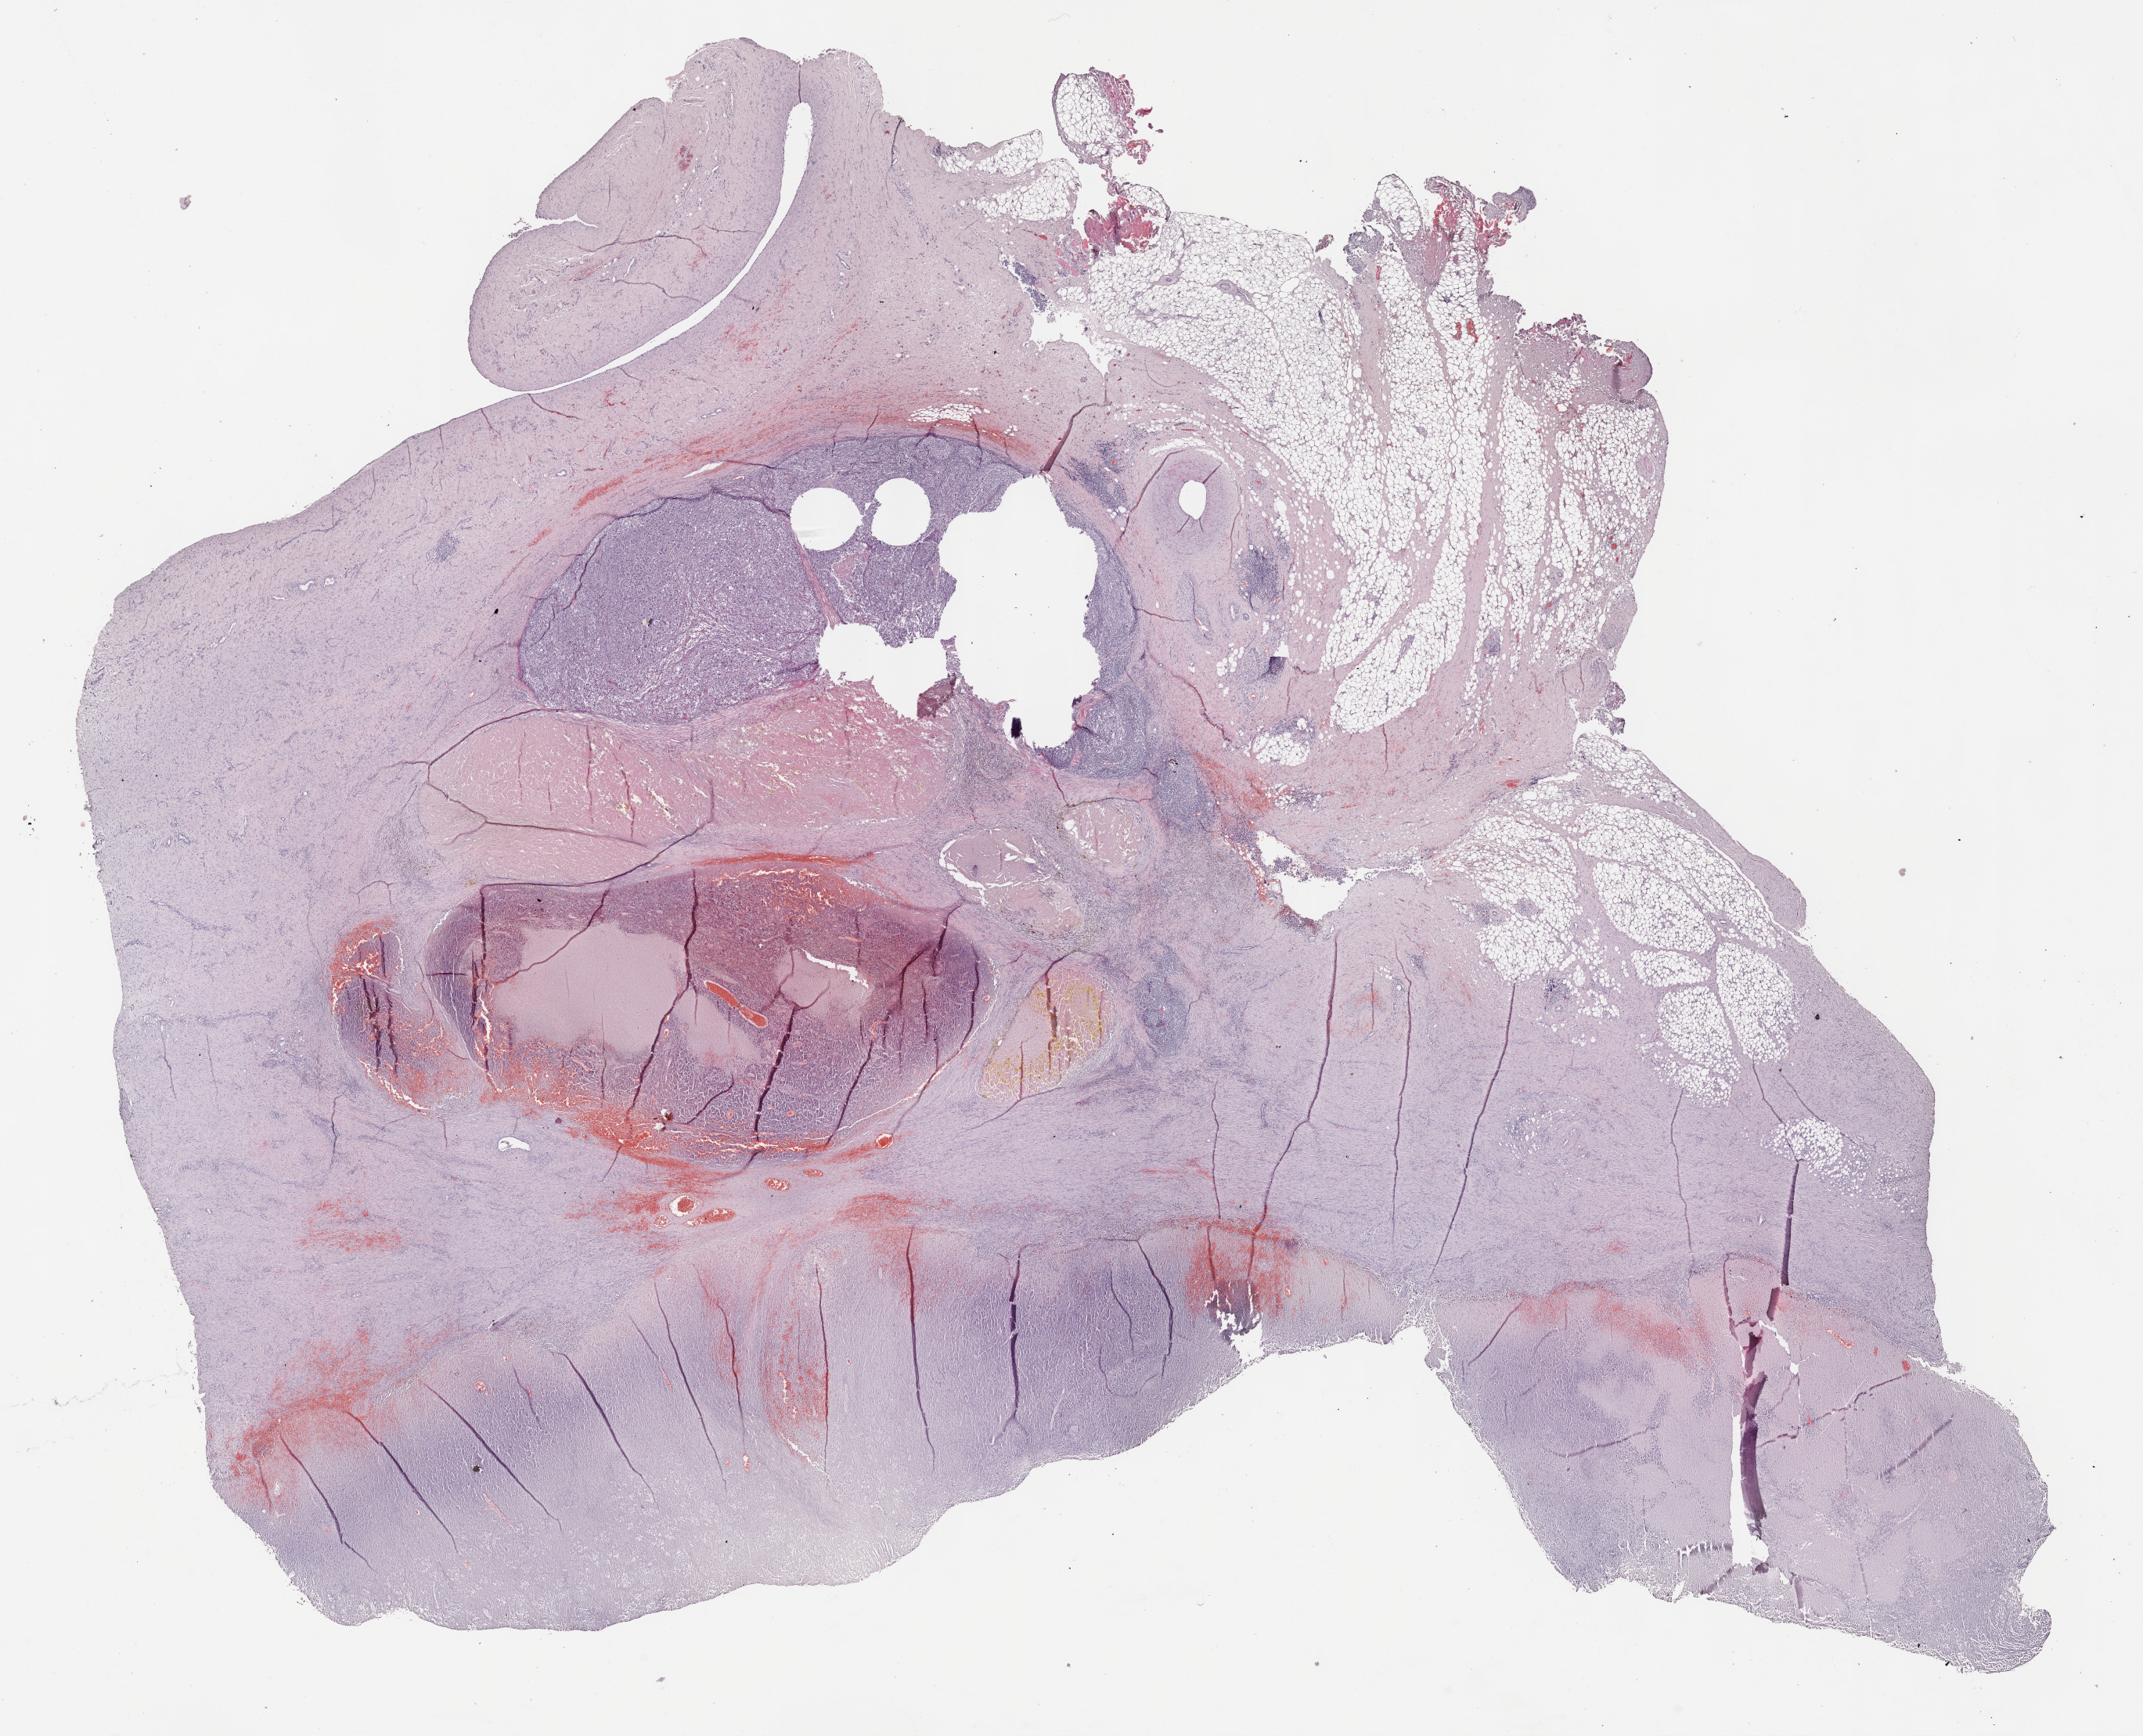
Whole-slide histology image, H&E — whole scanned area (about 22.1 x 17.9 mm) shown as a low-resolution overview. FFPE section. Sample: primary tumour, skin. Patient: male, age at initial diagnosis 71 years.
- pathologic diagnosis: Malignant melanoma, NOS